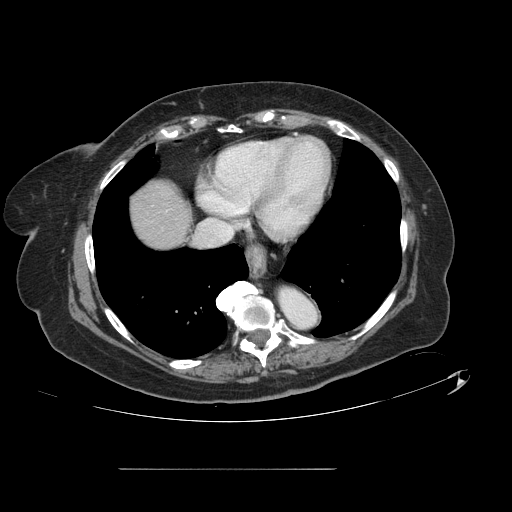
Contrast-enhanced abdominal CT, one axial slice; position 127 of 148 along the scan axis; intravenous contrast given; soft-tissue window (W 400 / L 40 HU); 512 × 512 image matrix. Female patient, age 75 years. Case-level facts recorded for this patient, not image findings: diagnosis: colorectal cancer liver metastases, imaged before liver resection; multiple liver metastases: no; largest metastasis: 2.4 cm; disease in both lobes: no.
Outlined on this slice (outlined manually by an expert reader):
- liver: box from (x=132, y=181) to (x=188, y=247) px
- planned liver remnant (the part of the liver to remain after resection): (x=132, y=181)–(x=189, y=247)